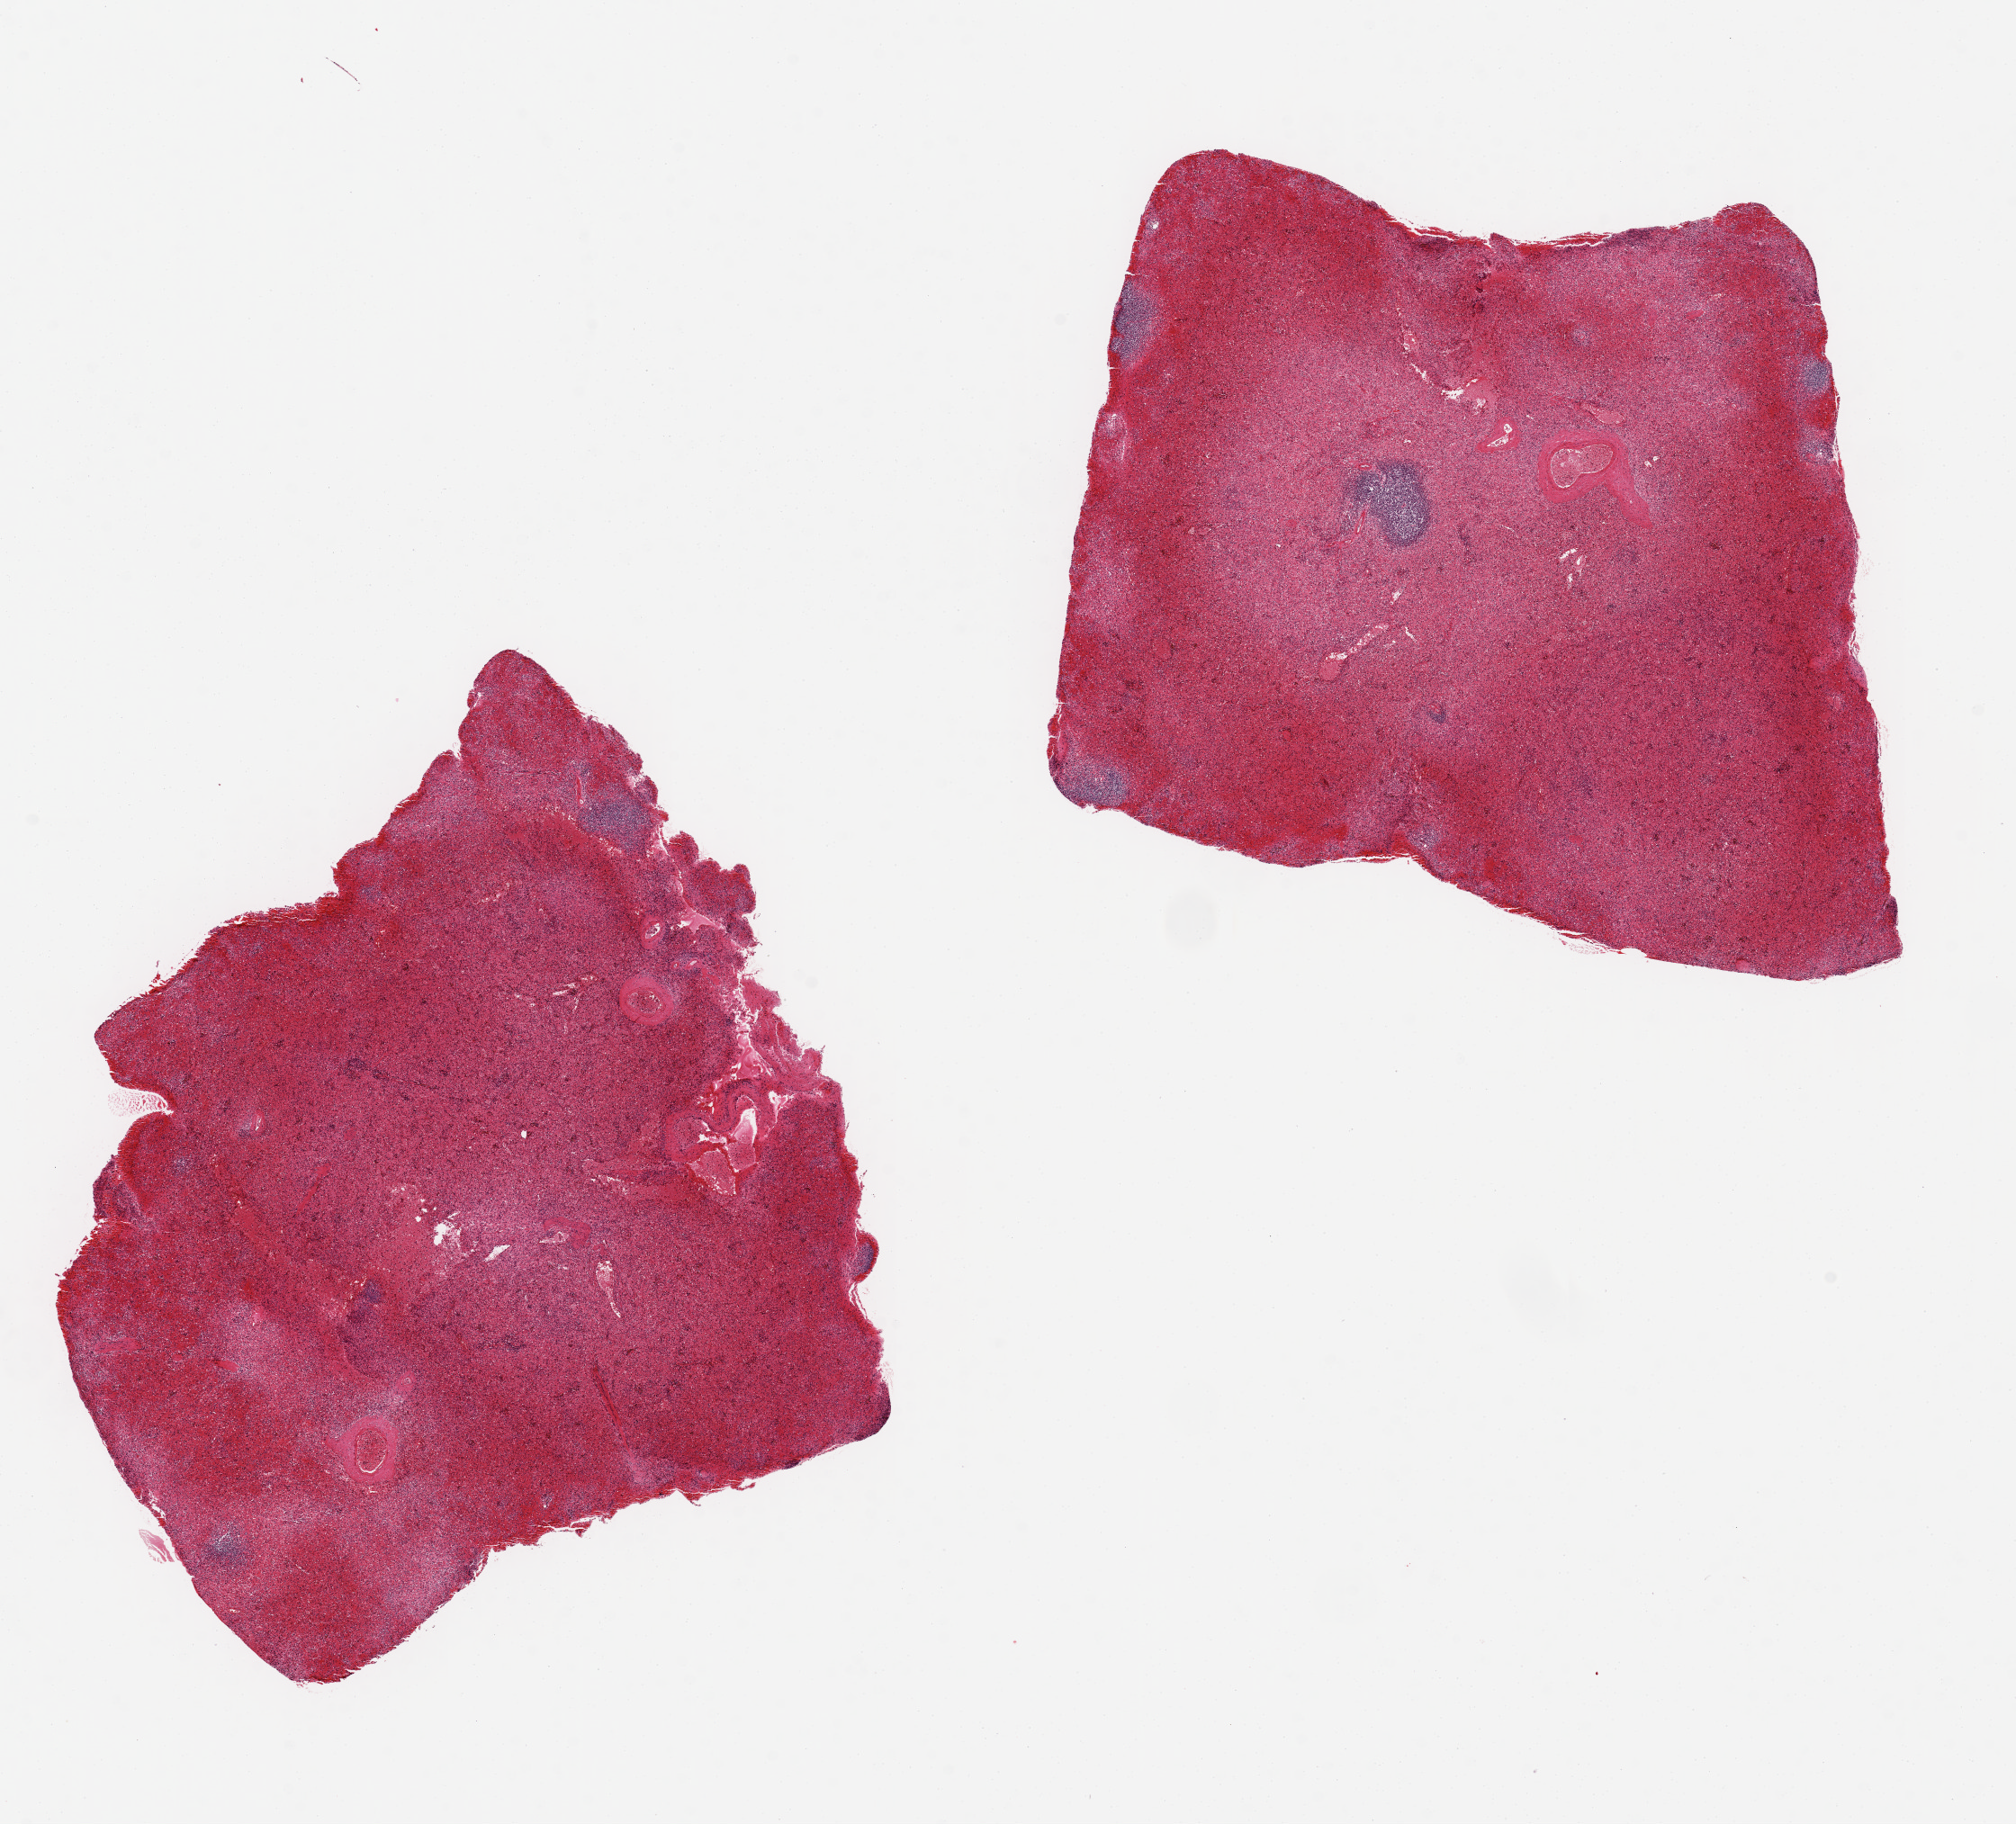
Digitized H&E-stained section — shown as a low-resolution overview of the whole scanned area (about 17.7 x 16.0 mm). PAXgene-fixed, paraffin-embedded tissue. Target tissue: spleen. Tissue donor sample. Donor: female.
Review note (as recorded): 2 pieces each 7x7 mm; moderately congested.